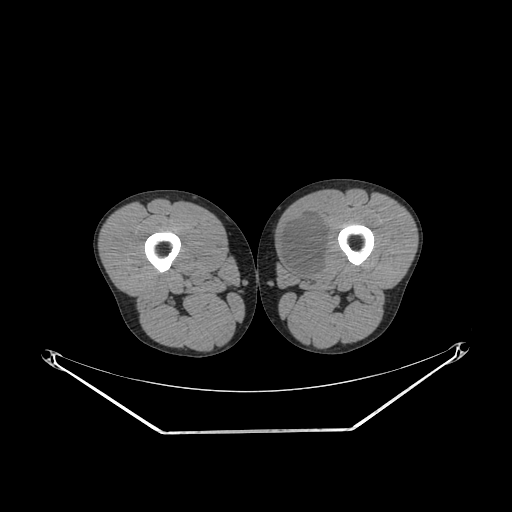
CT of an extremity soft-tissue mass (from a PET/CT study), one axial slice; slice 240 of 311 in the series (ordered by position); 140 kVp; soft-tissue window (W 400 / L 40 HU); 3.75 mm slice thickness; 512 × 512 image matrix, field of view 500 × 500 mm. Male patient. Case-level facts recorded for this patient, not image findings: histological type: mixoid liposarcoma; grade: low; site of the primary tumour: left thigh.
Outlined on this slice (expert contour drawn on MRI and transferred to this co-registered scan by the dataset authors):
- gross tumour volume (mass): box from (x=279, y=215) to (x=328, y=277) px